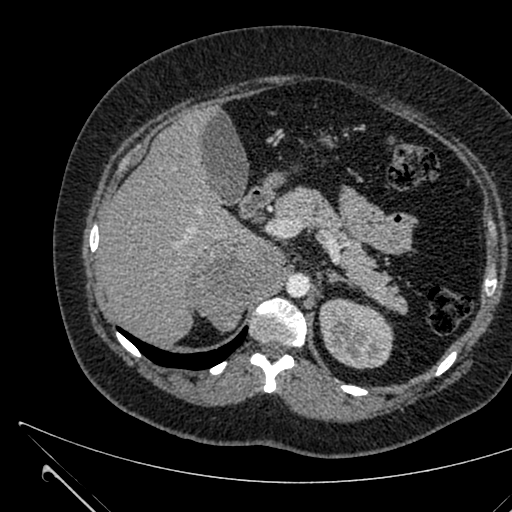
Contrast-enhanced abdominal CT, one axial slice; 120 kVp; intravenous contrast given; soft-tissue window (W 400 / L 40 HU); 512 × 512 image matrix. Female patient, age 36 years. From the clinical record (not read from this slice): diagnosis: adrenocortical carcinoma; tumour side: right adrenal; tumour size at pathology: 10 cm; Ki-67 index: 20 %; stage (as recorded): 4.
Annotated regions visible in this slice (semi-automatic segmentation, software-assisted and operator-edited):
- mass: bounding box [x1, y1, x2, y2] px = [191, 240, 282, 330]